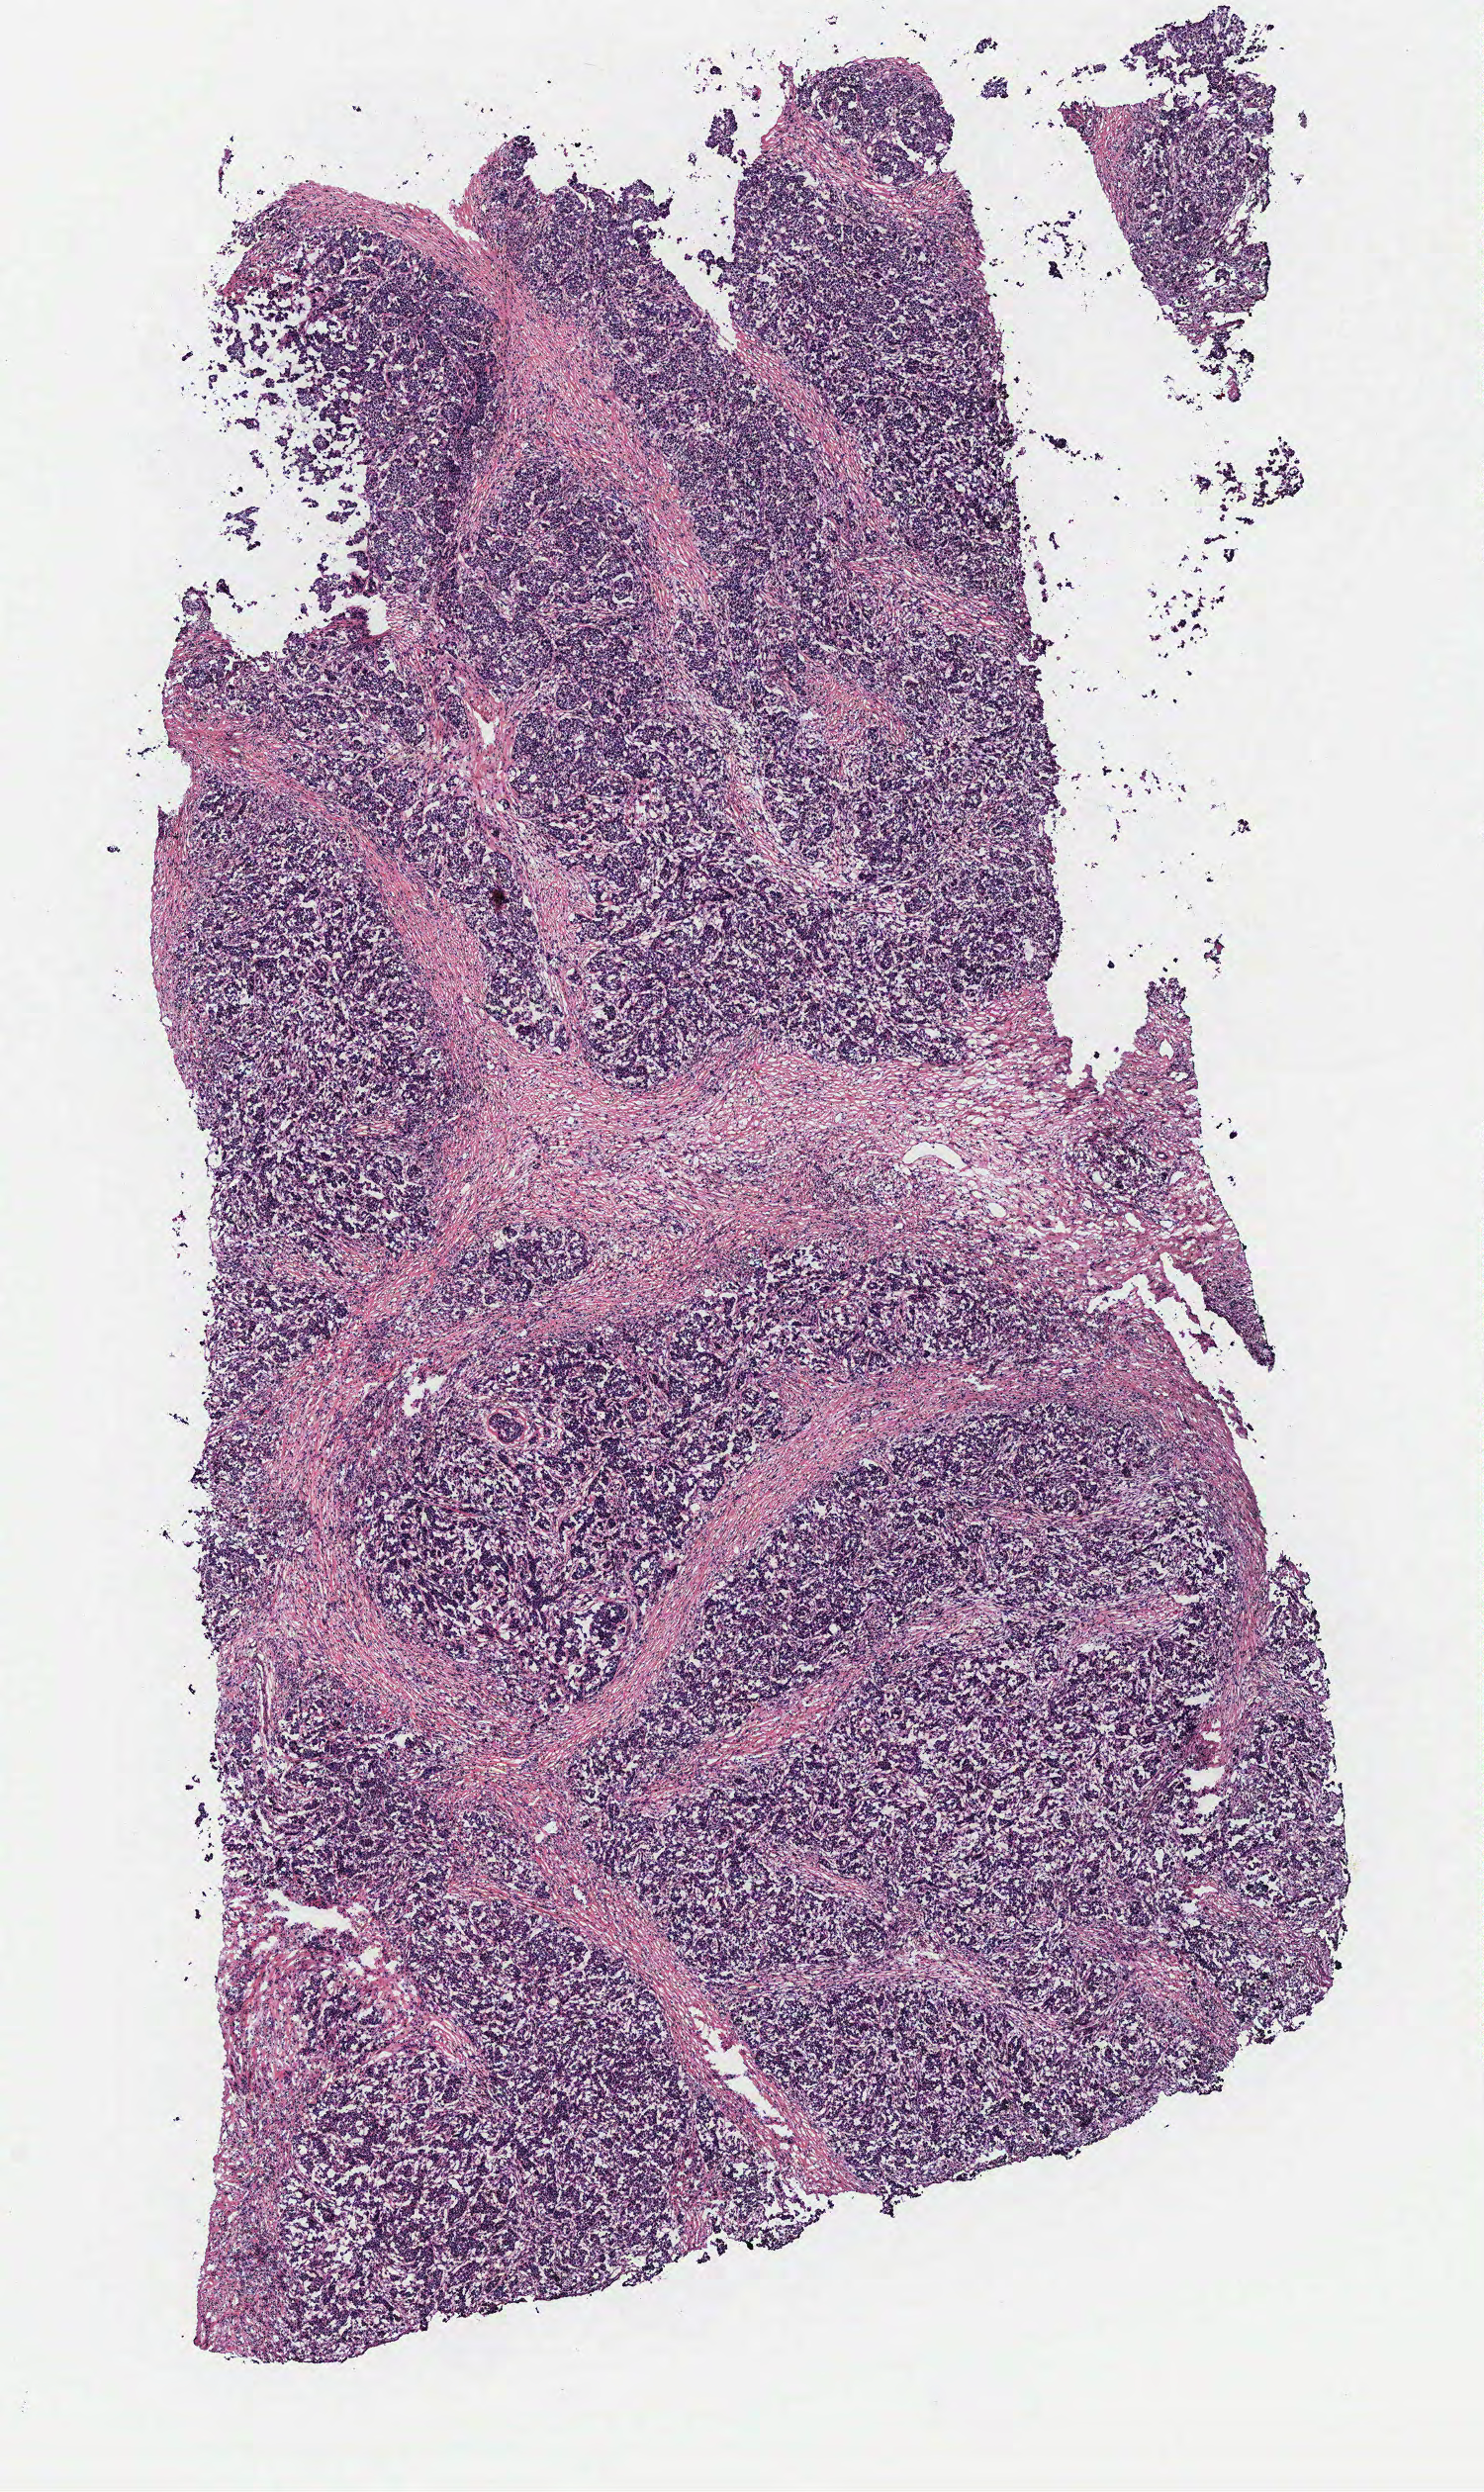
Whole-slide histology image, H&E, whole scanned area (about 6.0 x 10.1 mm, slide scanned at 40x) shown as a low-resolution overview. Female, 86 y/o.
Specimen: breast, tumour tissue.